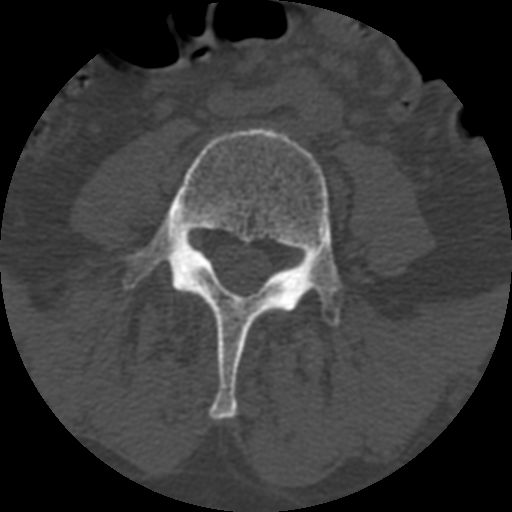
CT including the spine, one axial slice. Position 281 of 399 along the scan axis. Bone window (W 1800 / L 400 HU). 1.25 mm slice thickness. 512 × 512 image matrix, field of view 160 × 160 mm. Patient age 71 years. From the clinical record (not read from this slice): primary cancer: prostate.
Structures marked on this image (semi-automatically segmented with operator editing):
- L4 vertebra: box from (x=119, y=126) to (x=344, y=420) px